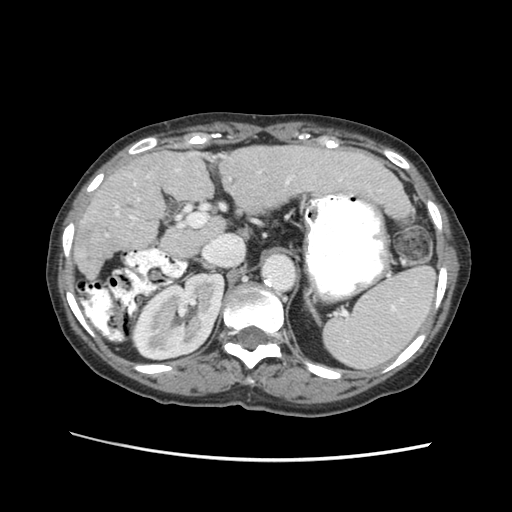
Contrast-enhanced abdominal CT (liver protocol), one axial slice. Position 34 of 63 along the scan axis. Soft-tissue window (W 400 / L 40 HU). 2.5 mm slice thickness. 512 × 512 image matrix, field of view 340 × 340 mm. Case-level facts recorded for this patient, not image findings: diagnosis: hepatocellular carcinoma (patient treated with transarterial chemoembolisation; whether this scan precedes or follows treatment is not stated here); TNM stage (as recorded): Stage-I; Child-Pugh class: B; tumour differentiation: well differentiated.
Outlined on this slice (semi-automatic segmentation, software-assisted and operator-edited):
- abdominal aorta: bounding box [x1, y1, x2, y2] px = [264, 255, 293, 289]
- liver parenchyma outside the tumour (the mass and vessels are separate outlines, so this box may not span the whole liver): [74, 141, 406, 278]
- liver vessels: [105, 152, 358, 237]